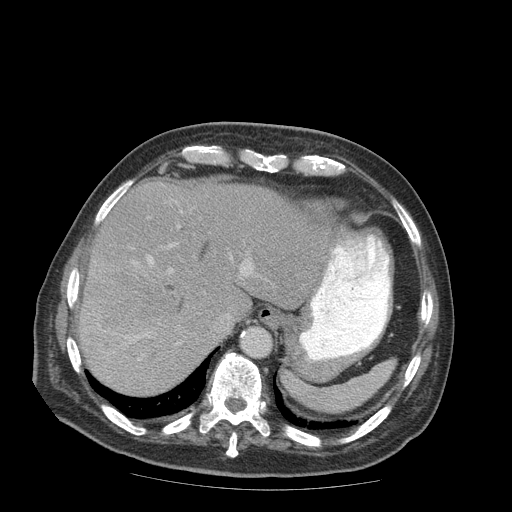
Contrast-enhanced abdominal CT (liver protocol), one axial slice. Slice 68 of 99 in the series (ordered by position). Reconstruction kernel STANDARD. Soft-tissue window (W 400 / L 40 HU). 512 × 512 image matrix. Case-level facts recorded for this patient, not image findings: diagnosis: hepatocellular carcinoma (patient treated with transarterial chemoembolisation; whether this scan precedes or follows treatment is not stated here); TNM stage (as recorded): Stage-IIIB; Child-Pugh class: A; tumour differentiation: well differentiated; tumour nodularity: multinodular.
Outlined on this slice (semi-automatic segmentation, software-assisted and operator-edited):
- liver parenchyma outside the tumour (the mass and vessels are separate outlines, so this box may not span the whole liver): box from (x=80, y=180) to (x=347, y=394) px
- mass: (x=85, y=257)–(x=175, y=339)
- liver vessels: (x=124, y=226)–(x=253, y=361)